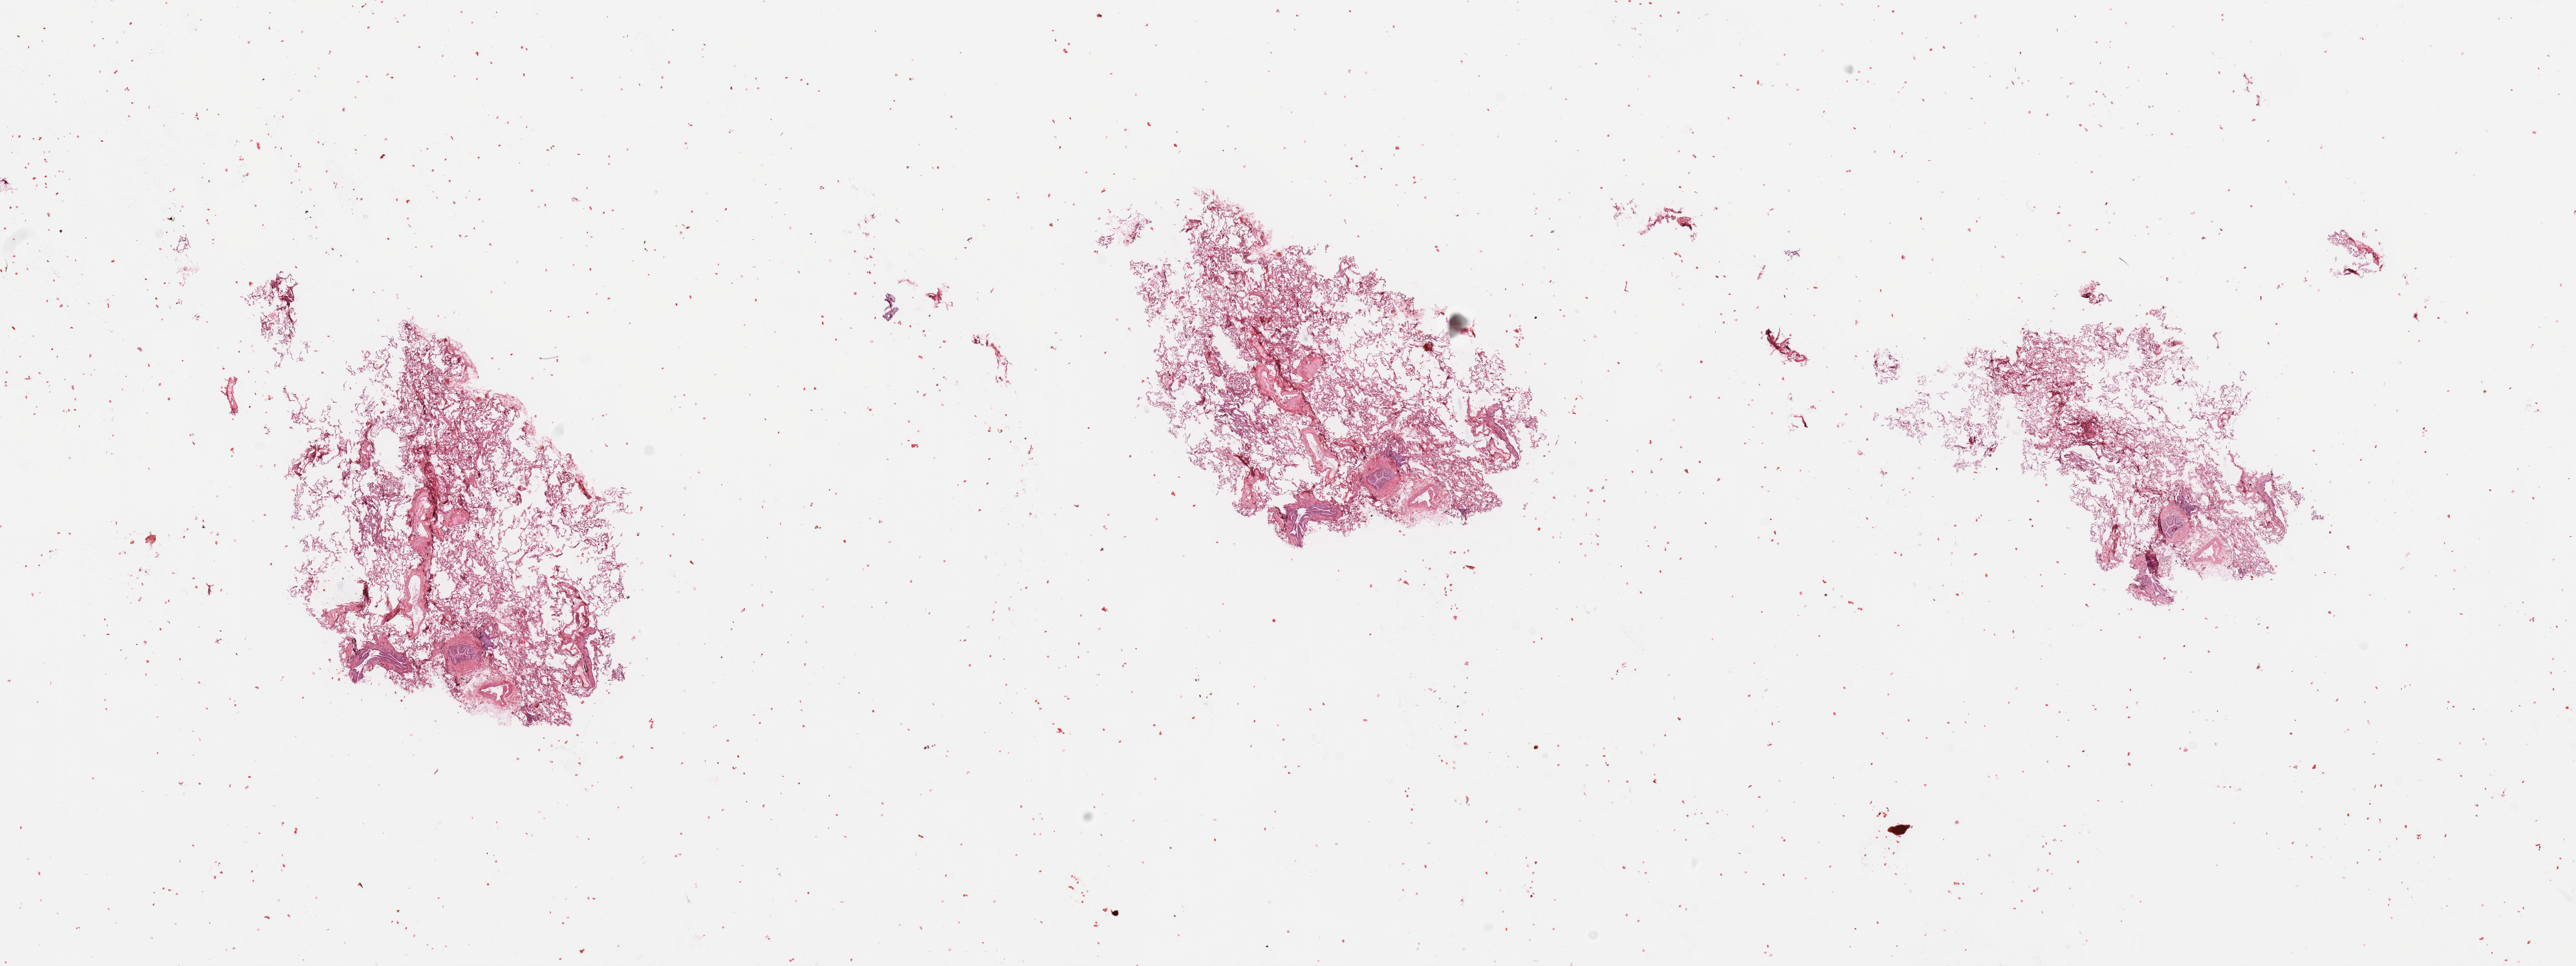
H&E-stained whole-slide image, a low-resolution overview of the entire scanned area, about 31.5 x 11.8 mm, normal (non-tumour) tissue sample, sampled site: lung. 63-year-old male patient.
This section: normal (non-tumour) tissue from the same patient. Patient diagnosis: Squamous cell carcinoma, NOS.